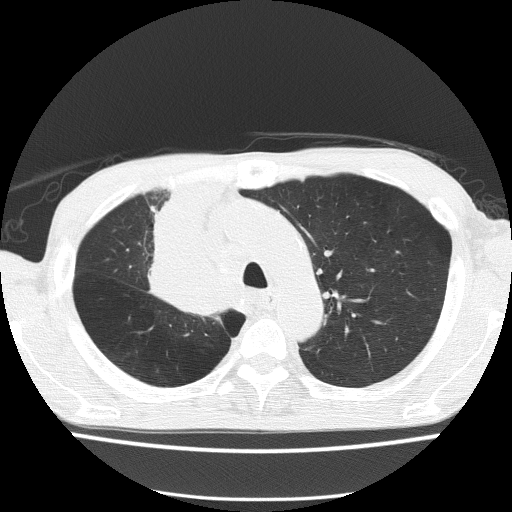
Low-dose screening chest CT, one axial slice. Position 110 of 150 along the scan axis. 120 kVp. Lung window (W 1500 / L -600 HU). 2 mm slice thickness. 512 × 512 image matrix, field of view 336 × 336 mm.
Structures marked on this image (expert manual segmentation):
- lesion 1 (tumor, hilum of right lung): bounding box (x1, y1, x2, y2) in pixels: (151, 183, 228, 313)